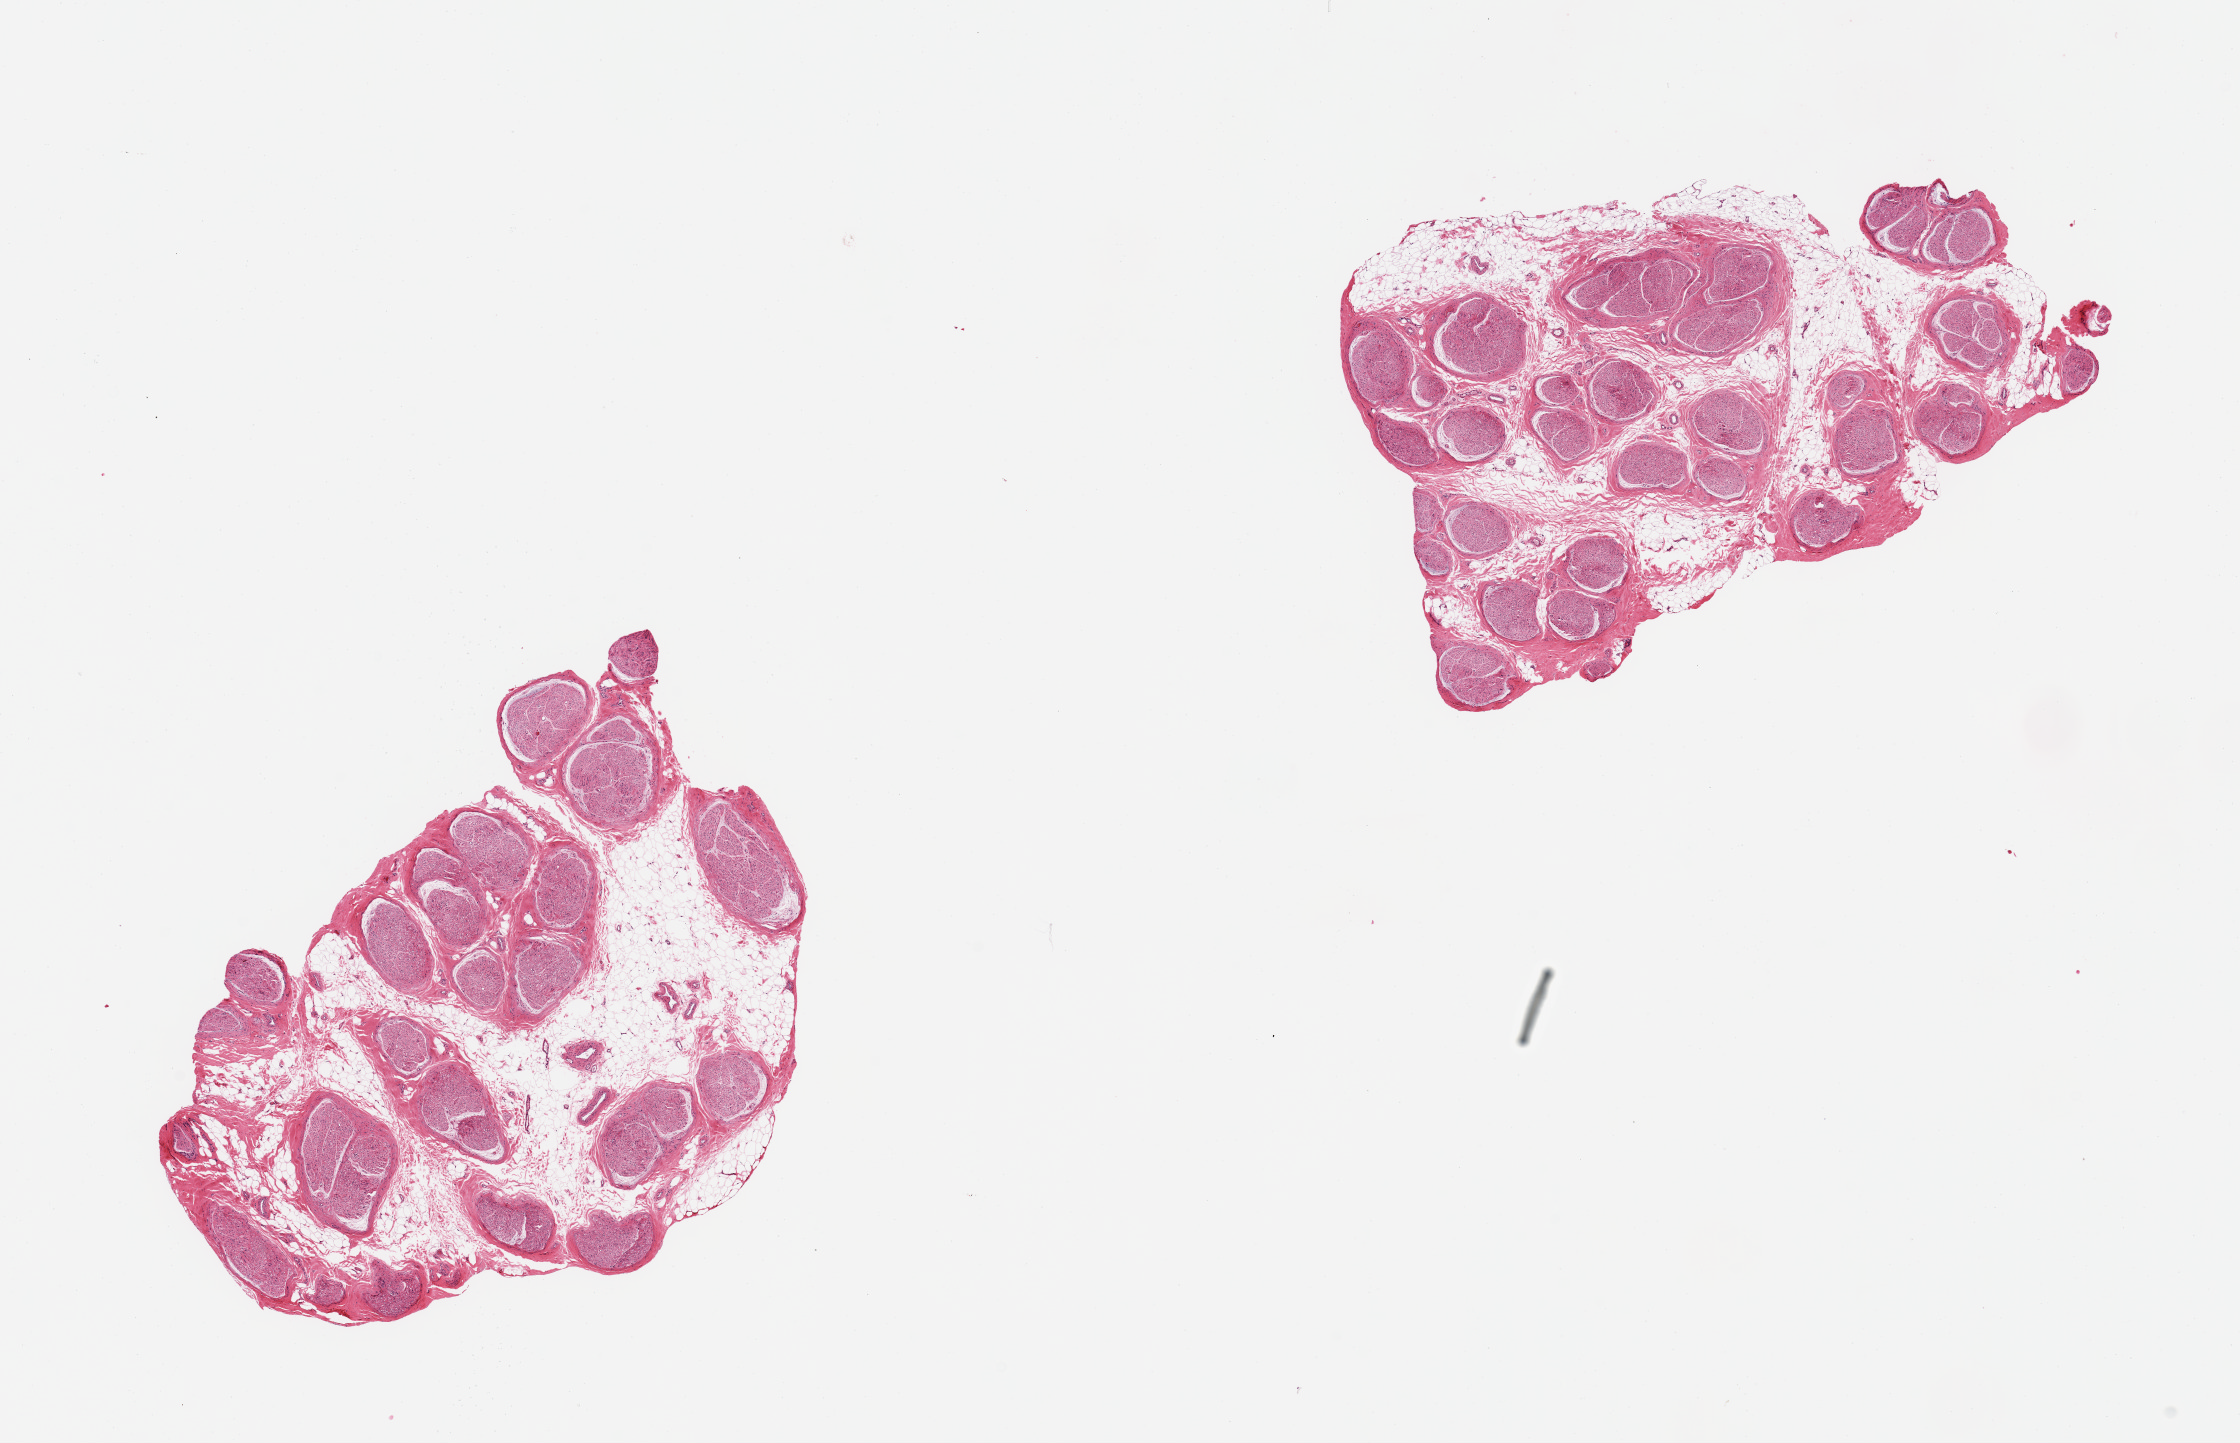
Whole-slide image, haematoxylin and eosin stain, a low-resolution overview of the entire scanned area, about 17.7 x 11.4 mm, PAXgene-fixed, paraffin-embedded tissue, target tissue: tibial nerve, tissue donor sample. Donor sex: male.
Pathologist's review note for this sample: 2 pieces, no adherent fat, ~30-40% interstitial fat.